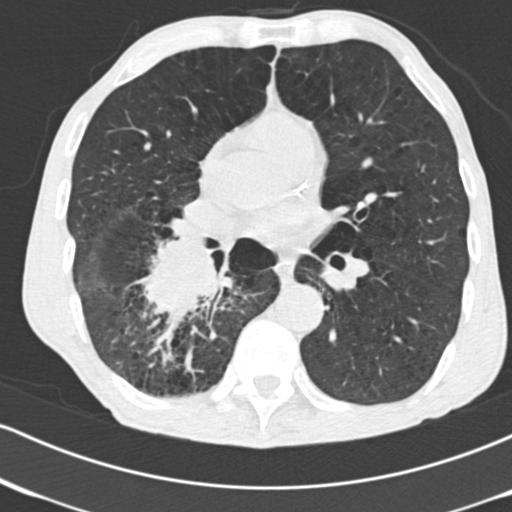
Low-dose screening chest CT, axial slice. Second annual screen. Lung window (W 1500 / L -600 HU). 2 mm slice thickness. Standard (soft-tissue) reconstruction kernel (B30f). Slice 99 of 182 in the series. Male, age 64 years at enrolment. Current smoker at enrolment.
• Expert-annotated lung lesion, bounding box (x1, y1, x2, y2) in pixels: (127, 227, 241, 334).
• Screening reader's record for this exam (one nodule recorded; not confirmed to be the boxed lesion): non-calcified nodule or mass ≥4 mm, 52 × 37 mm, spiculated (stellate) margins, soft tissue attenuation, pre-existing on the prior screen: no.